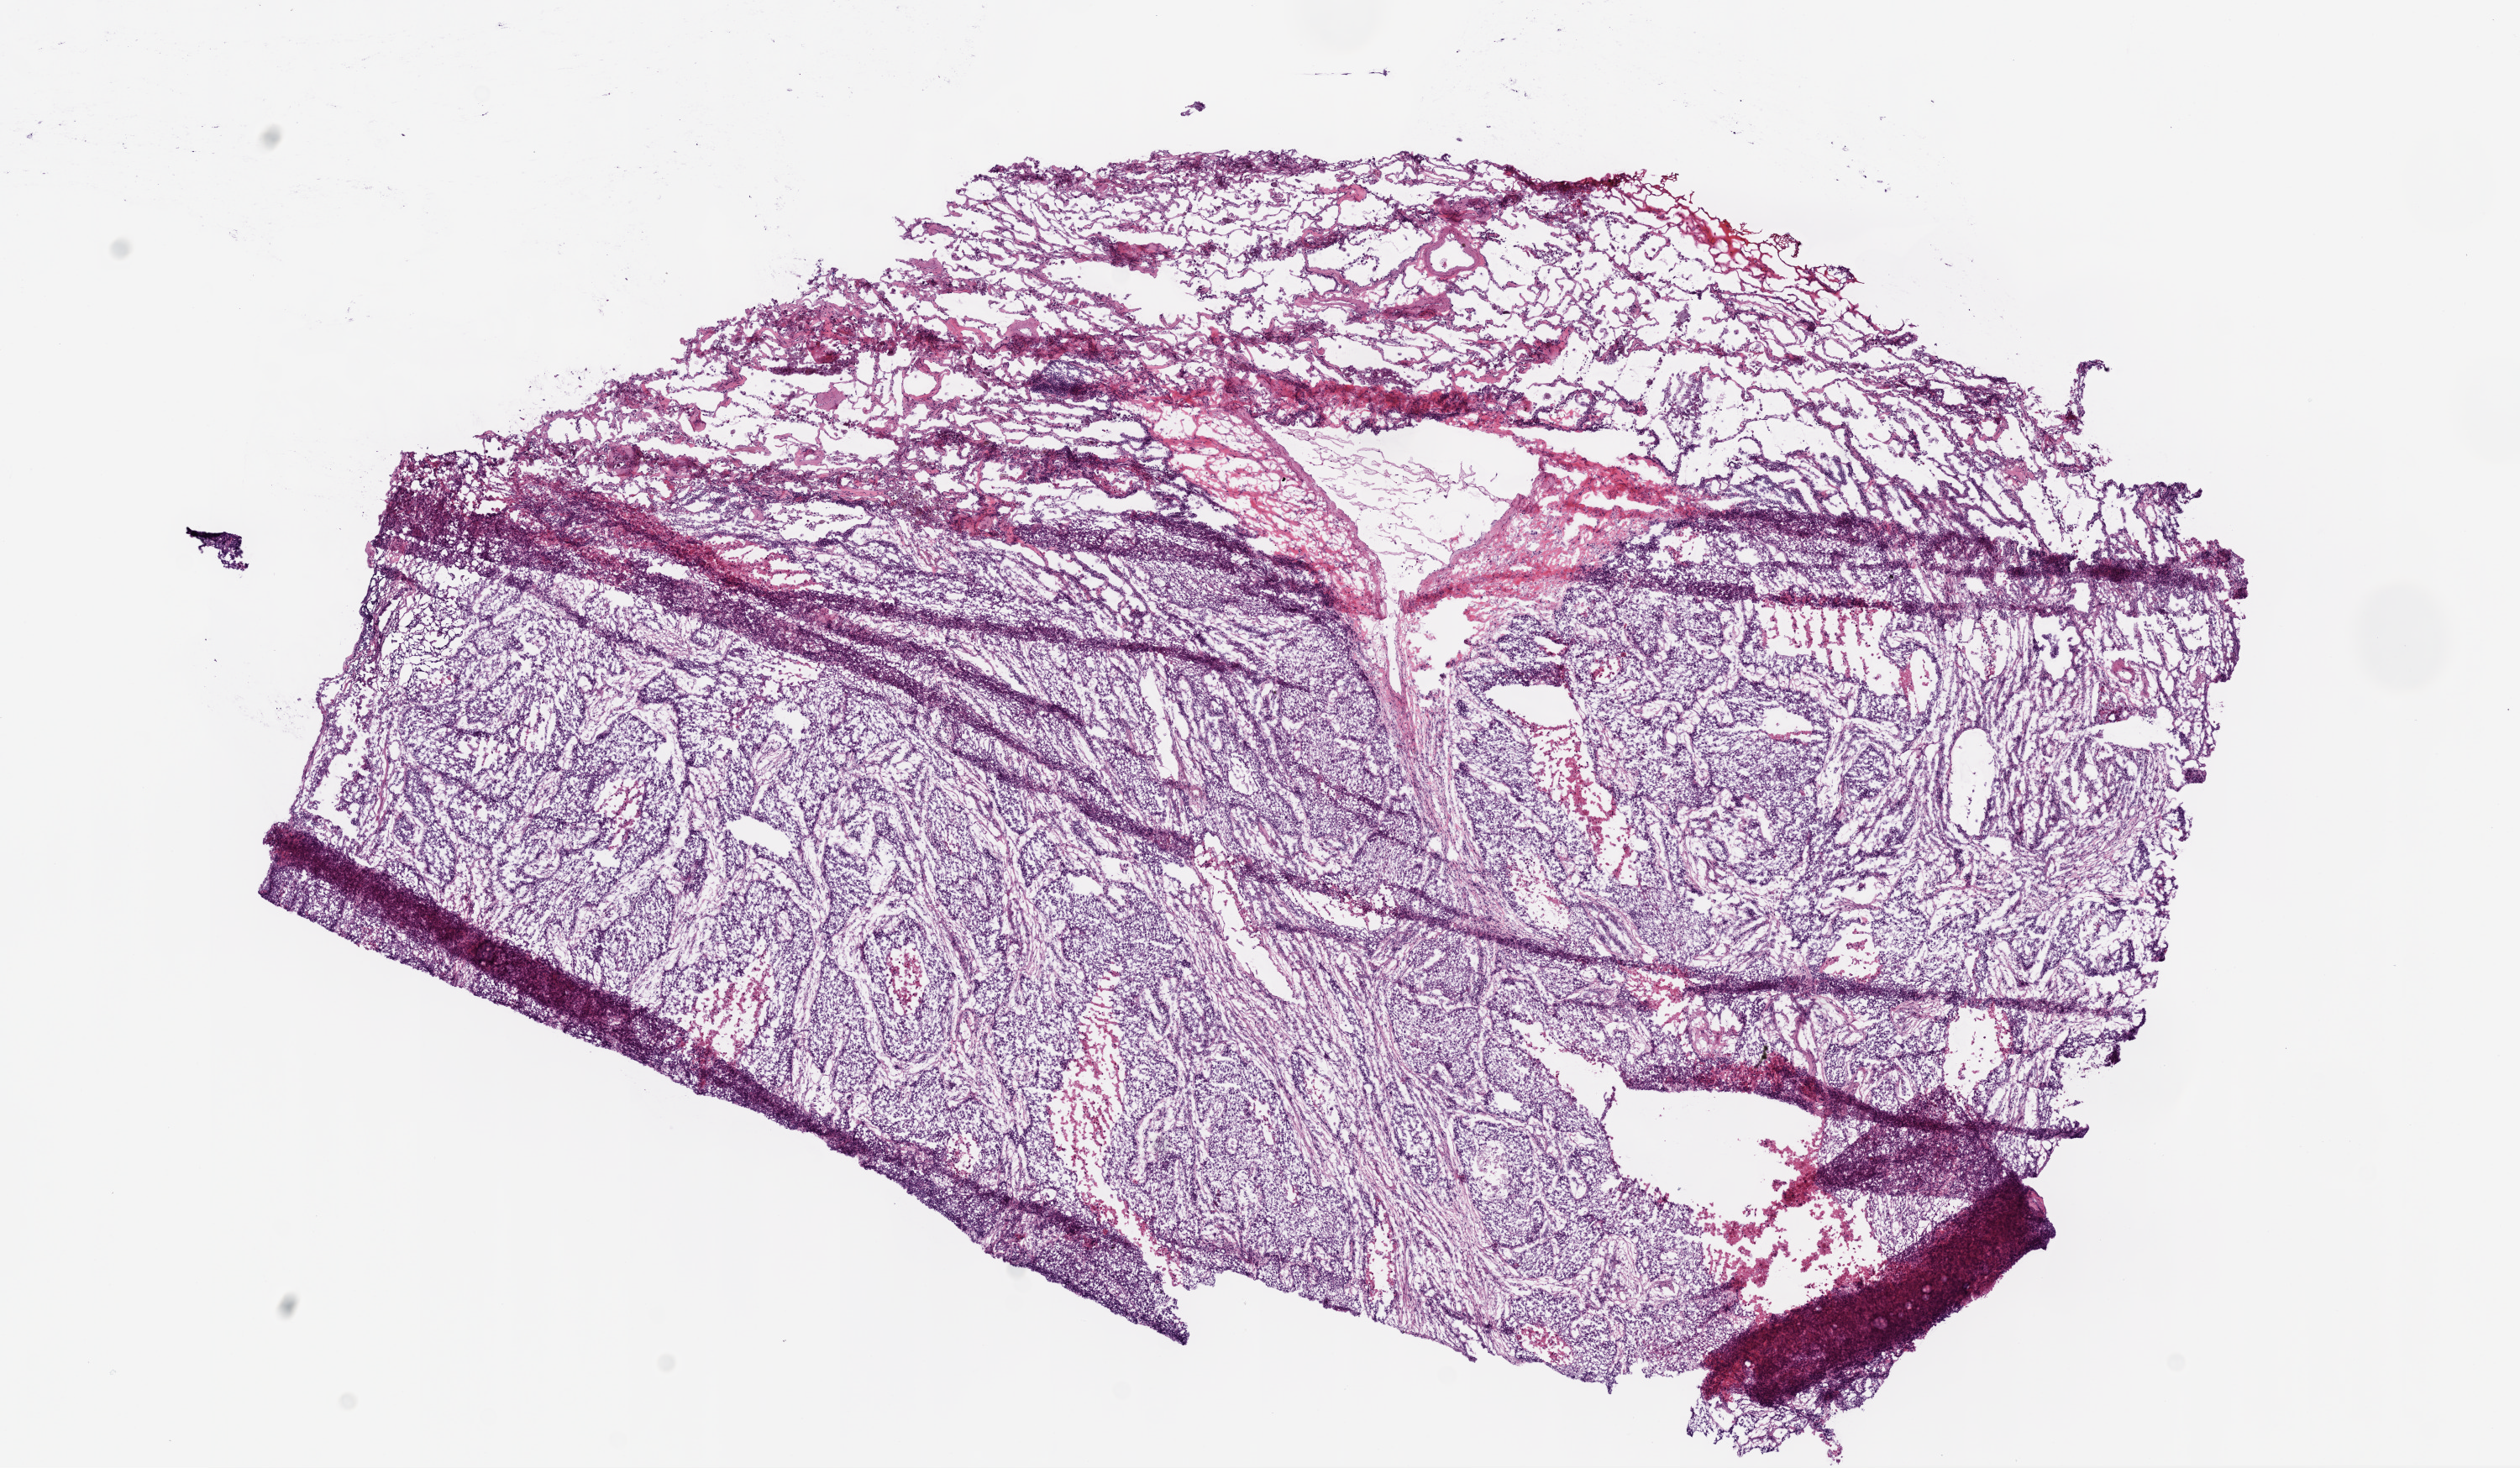
Digitized Hematoxylin and eosin (H&E) stained tissue section (whole slide), a low-resolution overview of the entire scanned area, about 12.0 x 7.0 mm. Frozen section. Lung, primary tumour sample. Female patient; age at initial diagnosis 64 years. Slide review estimates, as recorded: tumour cells 70%, tumour nuclei 85%, normal cells 20%, stromal cells 5%, necrosis 5%.
- diagnosis: Squamous cell carcinoma, NOS
- laterality: right
- AJCC pathologic stage: IB